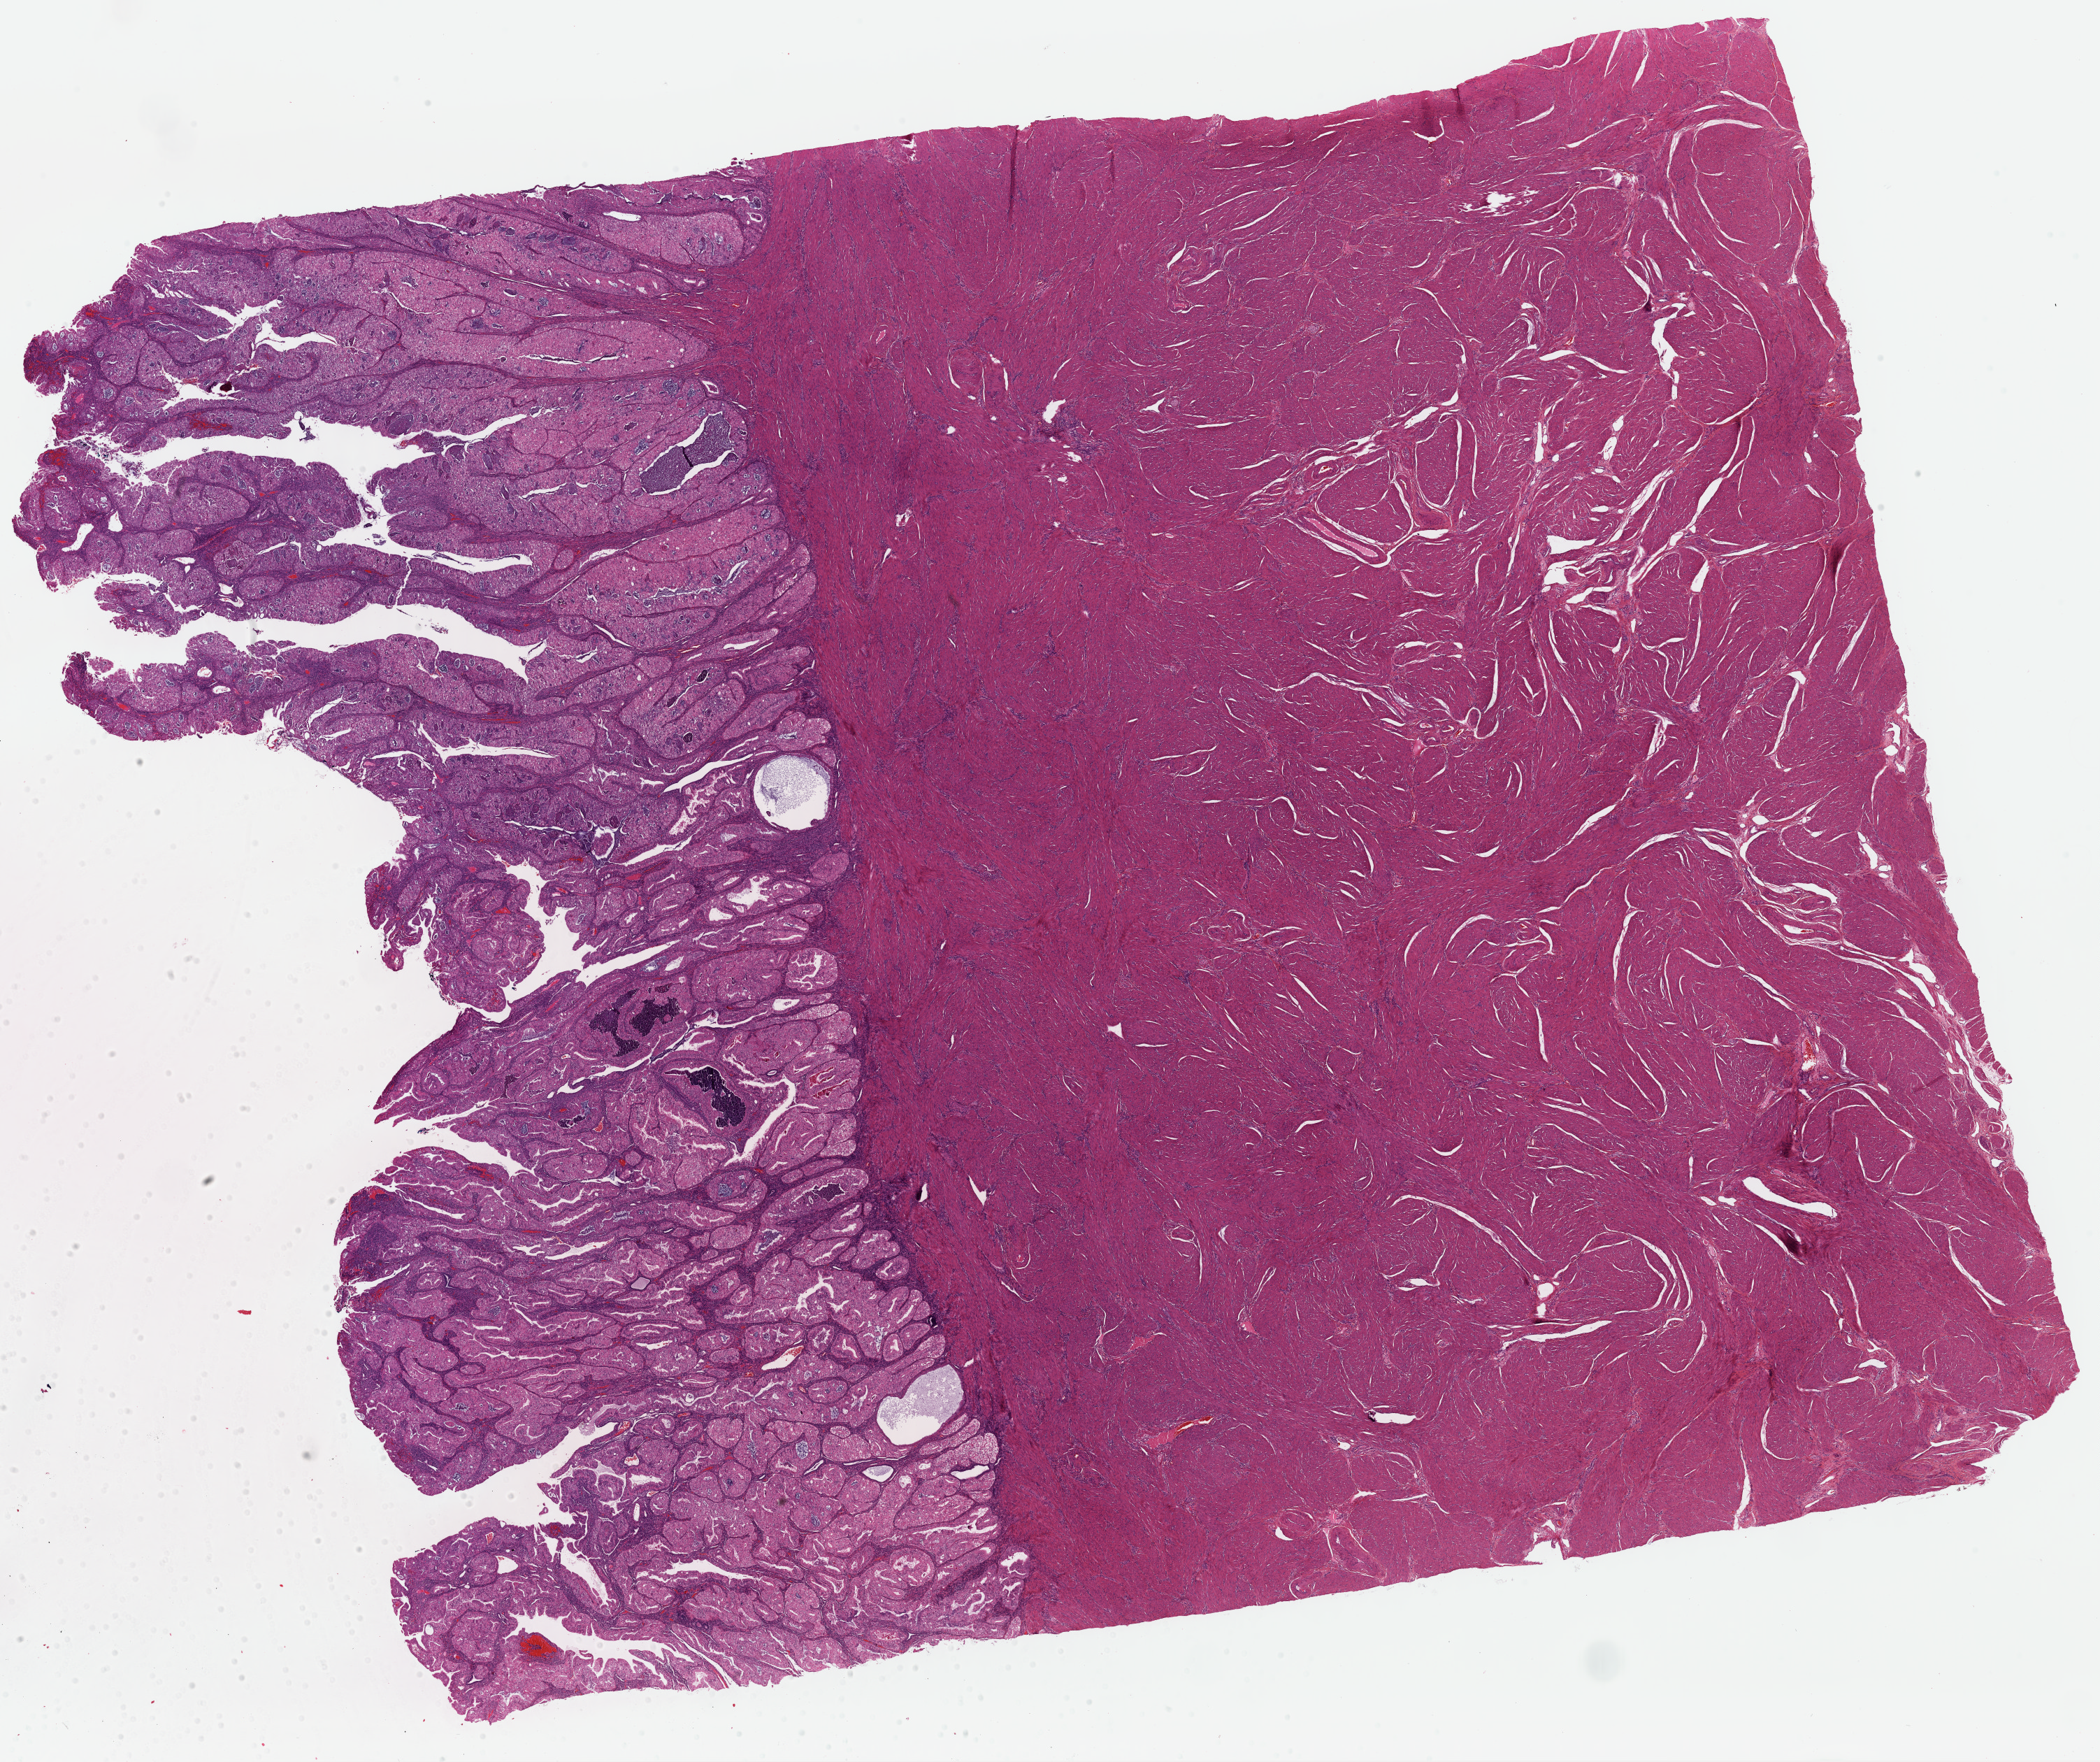
Digitized H&E tissue section (whole slide), a low-resolution overview of the entire scanned area, about 23.7 x 19.9 mm. Formalin-fixed paraffin-embedded (FFPE) diagnostic section. Primary tumour sample from the uterus. Female patient; age at initial diagnosis 31 years. Histologic grade: G2 (moderately differentiated).
• histologic diagnosis: Endometrioid adenocarcinoma, NOS
• FIGO stage: IA